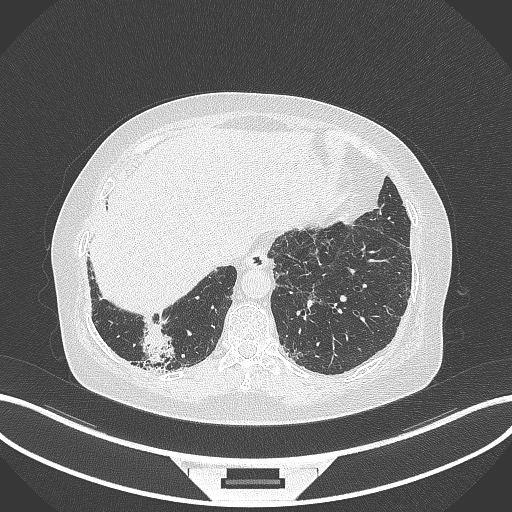
Chest CT, one axial slice; position 27 of 296 along the scan axis; lung window (W 1500 / L -600 HU); 512 × 512 image matrix, field of view 400 × 400 mm. Female patient, age 65 years. Case-level facts recorded for this patient, not image findings: clinical TNM (as recorded): T2b N1 M0; histopathological grade: G1.
Annotated regions visible in this slice (rectangle marked by the reading radiologist):
- lung tumour (recorded histology: adenocarcinoma): bounding box (x1, y1, x2, y2) in pixels: (138, 322, 177, 365)